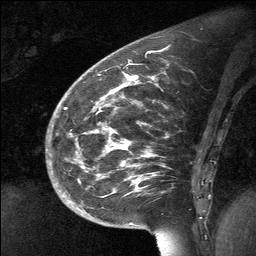
Breast MRI (dynamic contrast-enhanced), one sagittal slice. Slice 23 of 64 in the series (ordered by position). Dynamic contrast-enhanced study with each time point stored as its own series, time point 2 of 3 at this slice position (early post-contrast, ordered by acquisition time). 1.5 T. TE 4.8 ms, TR 27 ms. 2 mm slice thickness. 256 × 256 image matrix, field of view 200 × 200 mm. Patient: female, 39 years. Case-level facts recorded for this patient, not image findings: setting: breast cancer imaged before/during neoadjuvant chemotherapy; receptor status: HER2-positive.
Annotated regions visible in this slice (semi-automatic segmentation, software-assisted and operator-edited):
- analysis volume of interest (the breast-tissue region the enhancement analysis was run in; not a lesion): bounding box <70,69,202,224> (left, top, right, bottom; pixels)
- tumour enhancement mask (voxels above the 90 % enhancement threshold inside the analysis volume of interest): <96,76,138,182>